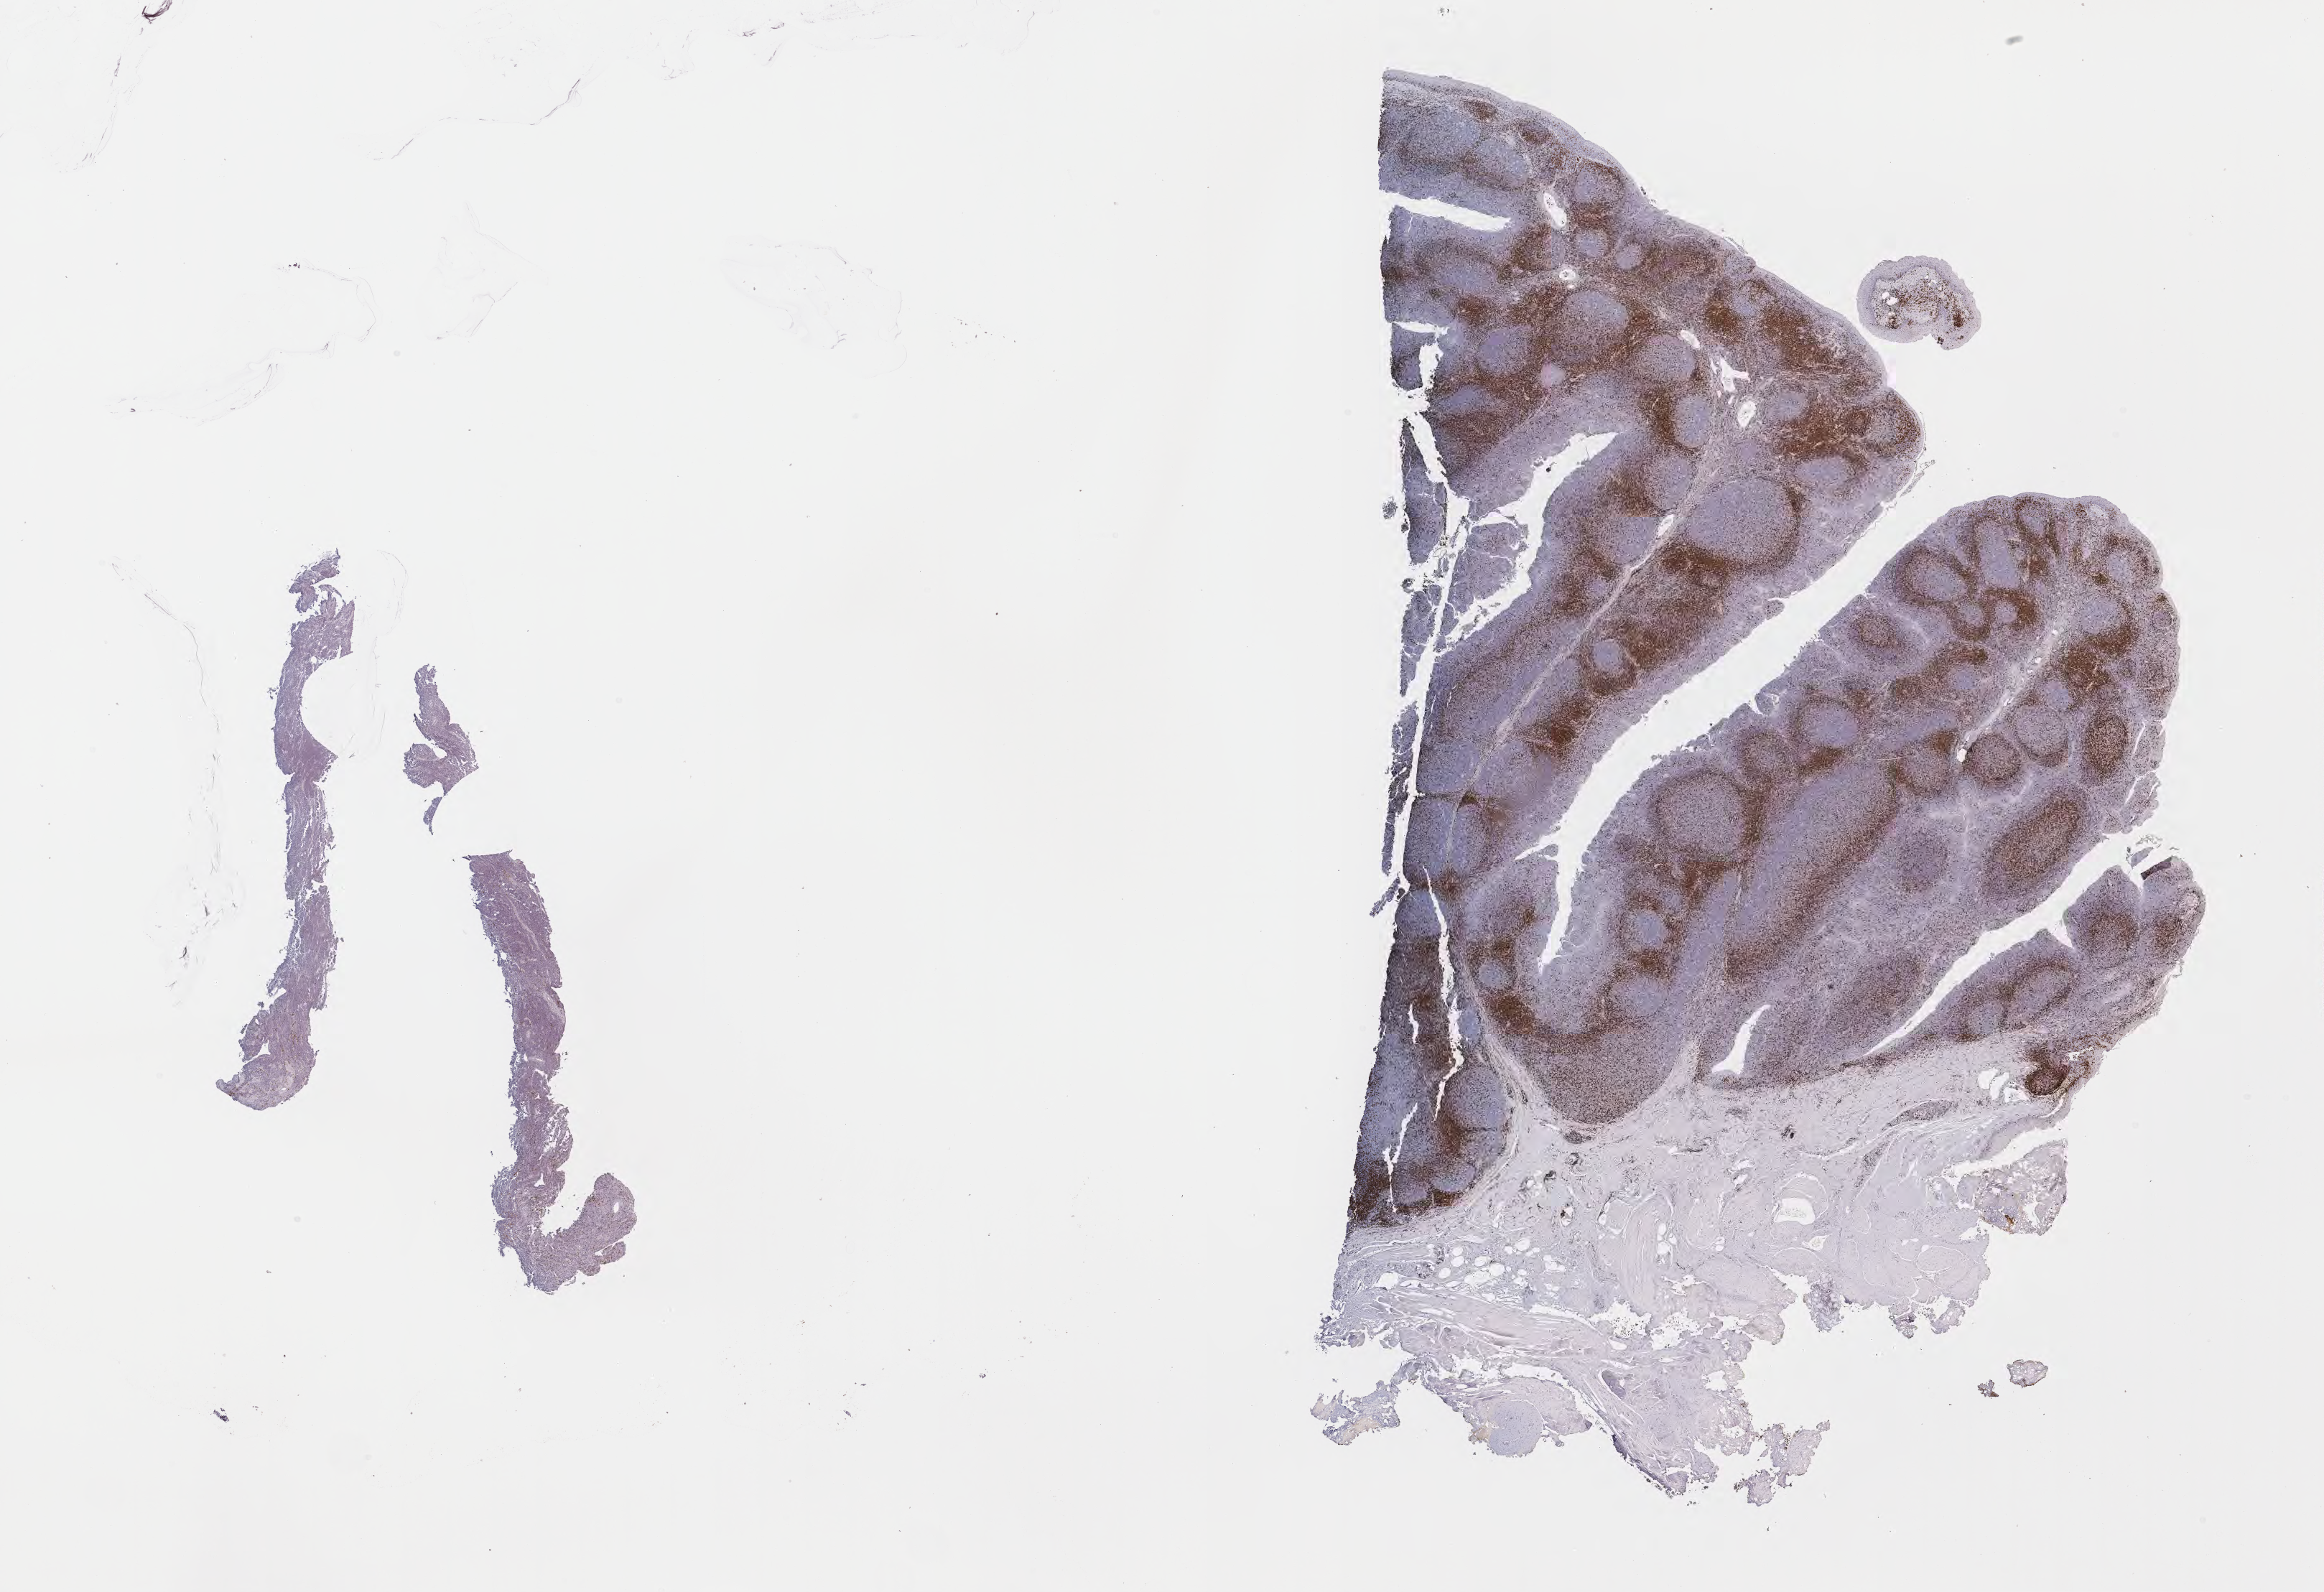
IHC for CD3, whole-slide image, shown as a low-resolution overview of the whole scanned area (about 26.2 x 17.9 mm), tumor tissue, site: spleen. Male, age 6 years at initial diagnosis.
* diagnosis: Burkitt lymphoma, NOS